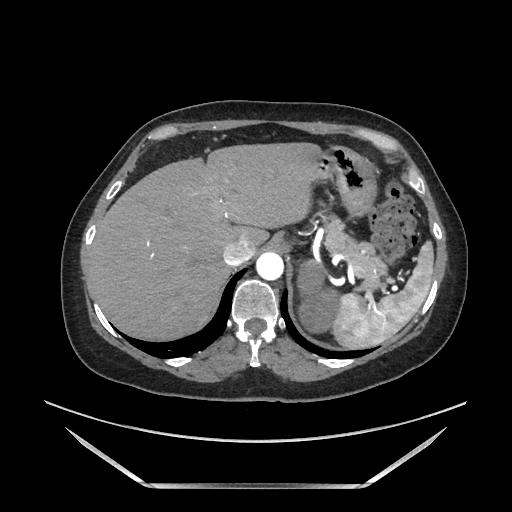
Contrast-enhanced abdominal CT, one axial slice; position 144 of 205 along the scan axis; soft-tissue window (W 400 / L 40 HU); 1.25 mm slice thickness; 512 × 512 image matrix, field of view 440 × 440 mm. Female patient. From the clinical record (not read from this slice): diagnosis: adrenocortical carcinoma; tumour side: left adrenal; tumour size at pathology: 12.5 cm; Ki-67 index: 39 %; stage (as recorded): 3.
Annotated regions visible in this slice (semi-automatically segmented with operator editing):
- mass: bounding box (x1, y1, x2, y2) in pixels: (300, 264, 334, 331)